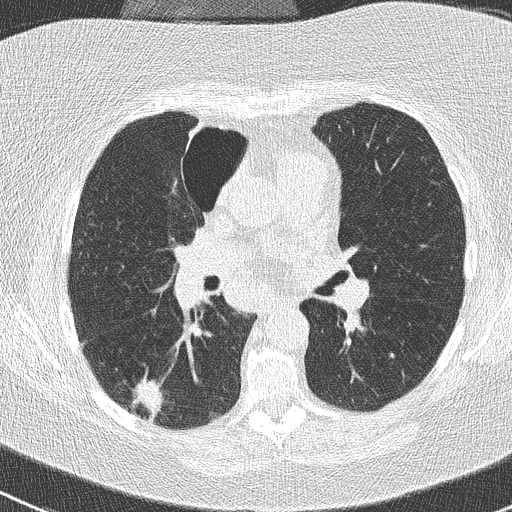
Chest CT (low-dose screening protocol), one axial image; baseline screening round; lung window (W 1500 / L -600 HU); 120 kVp; slice 118 of 261 in the series. Female participant, aged 74 years at enrolment. Former smoker at enrolment.
Expert-annotated lung lesion, box from (x=119, y=375) to (x=174, y=429) px. The screening reader recorded 3 non-calcified nodules or masses ≥4 mm on this exam (right lower lobe, right upper lobe, left lower lobe); which of them this box marks is not recorded. Participant outcome: lung cancer diagnosed 16 days after this screen — non-small cell carcinoma, right lower lobe, poorly differentiated (G3), stage IIIA (AJCC 6th edition), 28 mm at pathology.